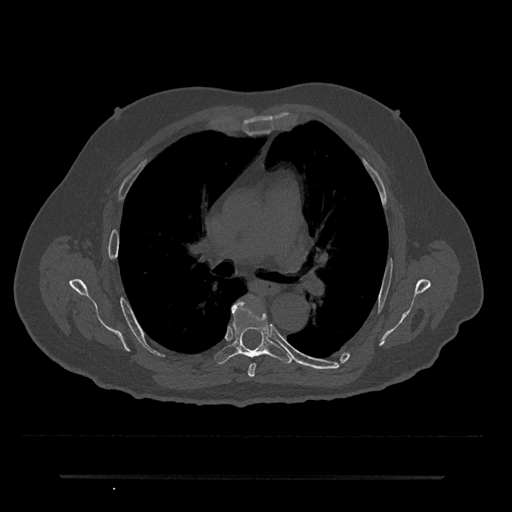
CT including the spine, one axial slice. Position 448 of 797 along the scan axis. Bone window (W 1800 / L 400 HU). 0.5 mm slice thickness. 512 × 512 image matrix, field of view 437 × 437 mm. Male patient, age 69 years. From the clinical record (not read from this slice): primary cancer: prostate.
Structures marked on this image (semi-automatically segmented with operator editing):
- T5 vertebra: box from (x=248, y=363) to (x=256, y=377) px
- T6 vertebra: (x=215, y=300)–(x=293, y=364)